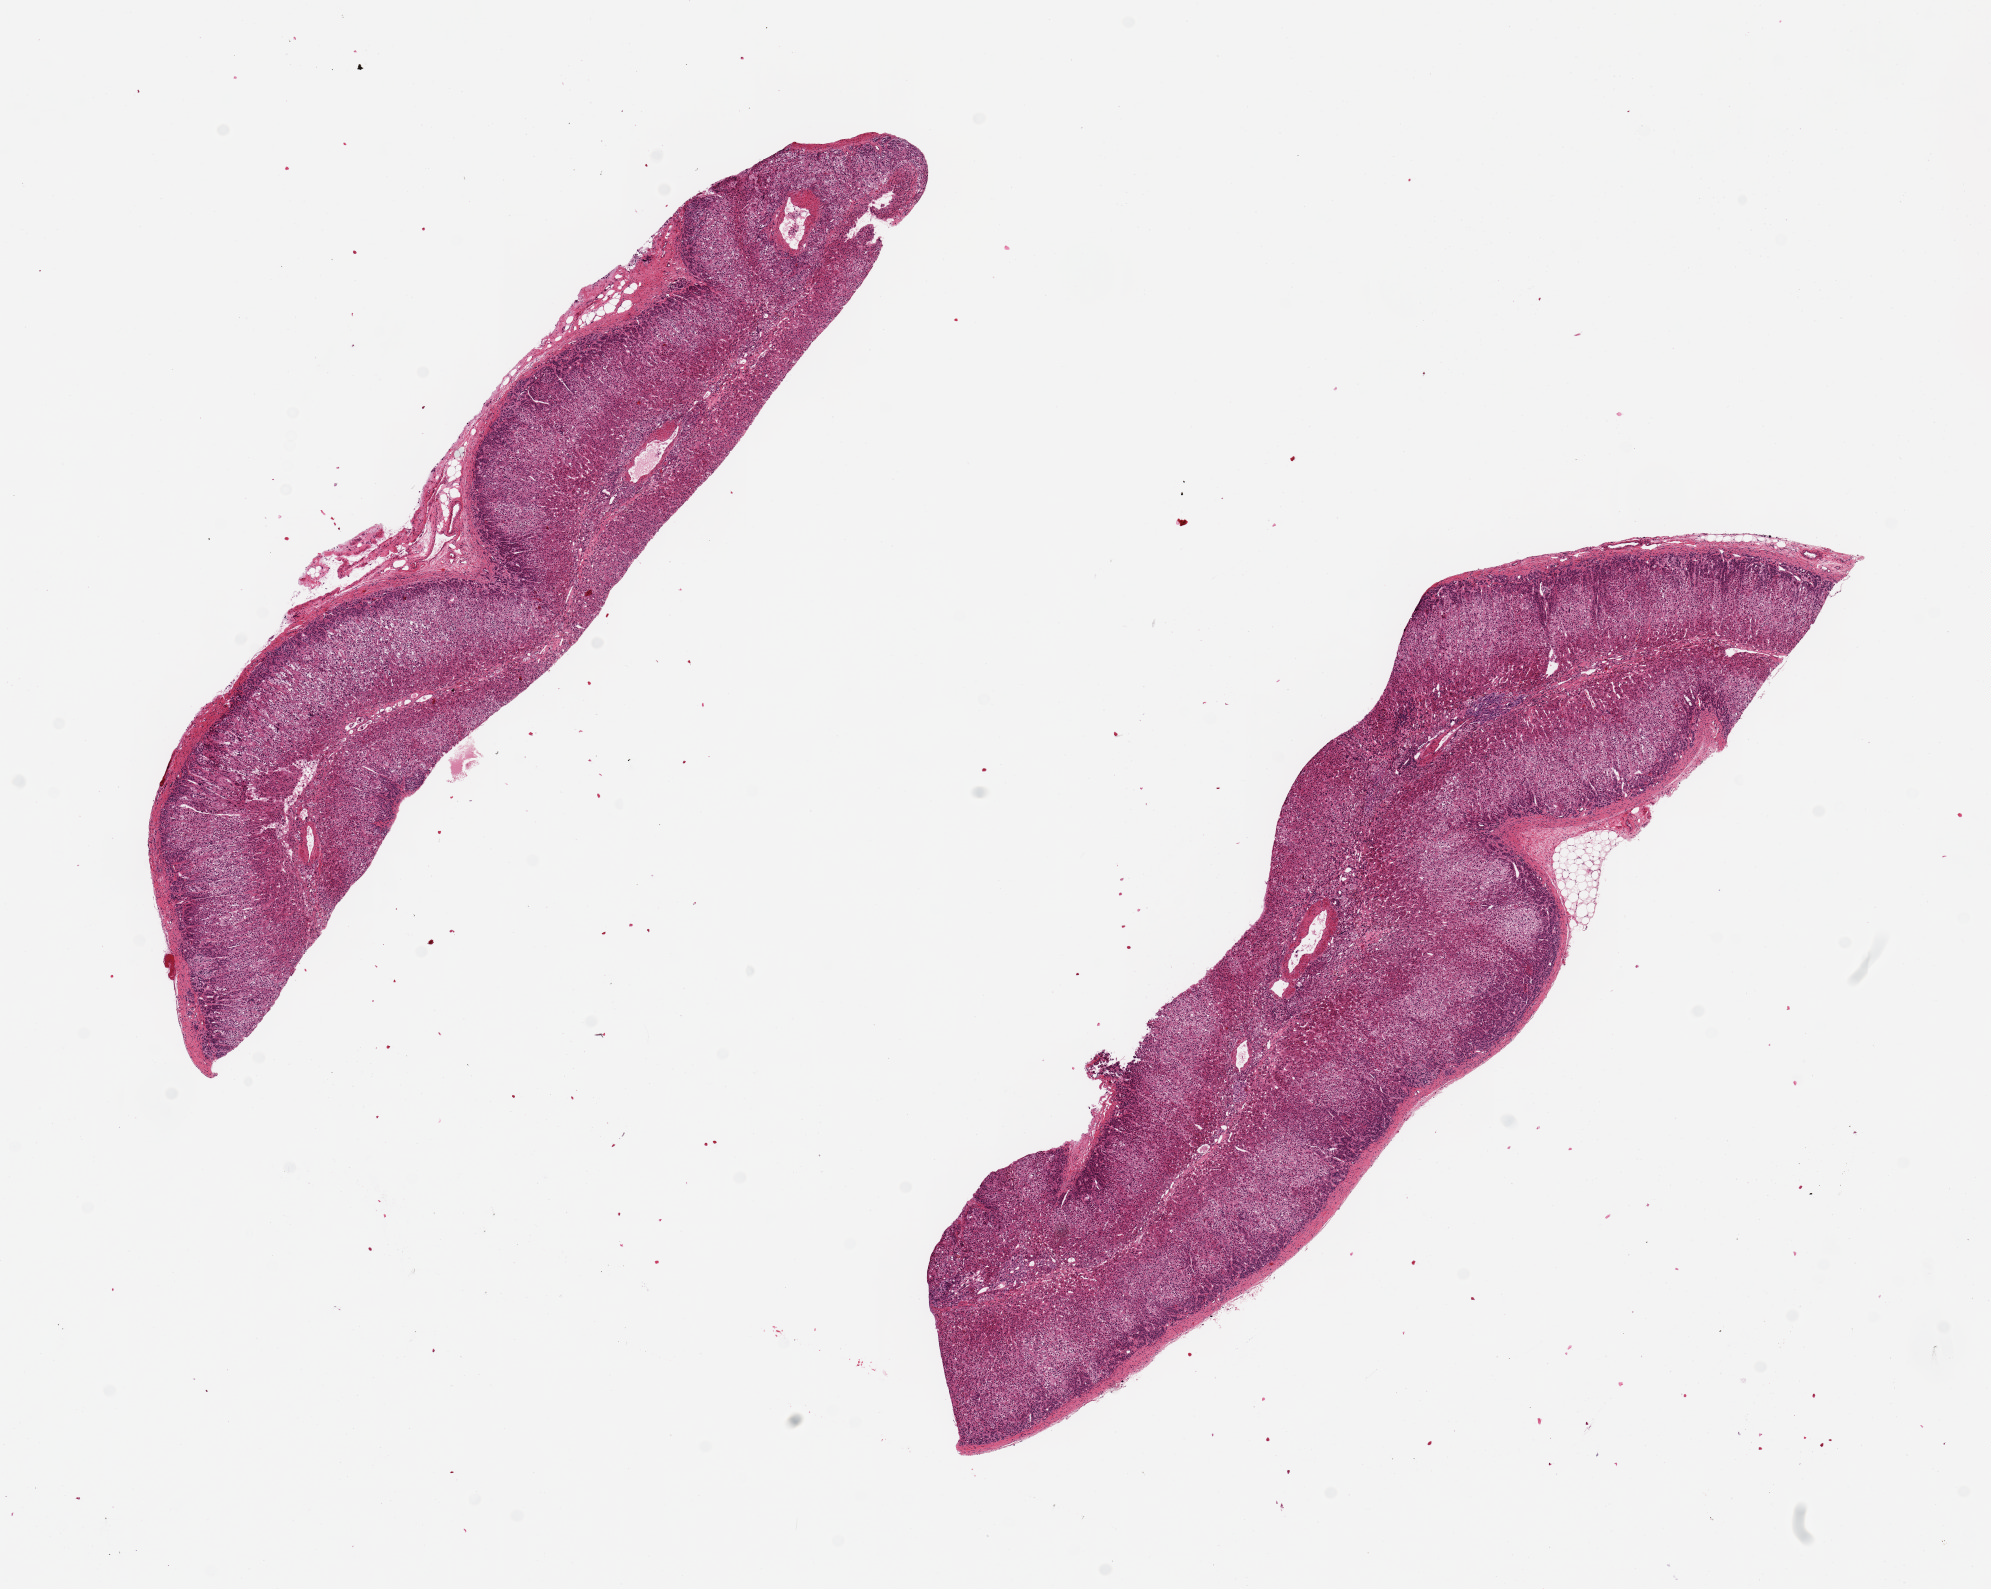
Digitized hematoxylin and eosin (H&E)-stained section, shown as a low-resolution overview of the whole scanned area (about 15.8 x 12.6 mm); PAXgene-fixed, paraffin-embedded tissue; target tissue: adrenal gland; tissue donor sample. Donor: male.
Pathologist's review note for this sample: 2 pieces 9.8x2.6 & 9x1.7 mm; mostly cortex; minimal adipose.